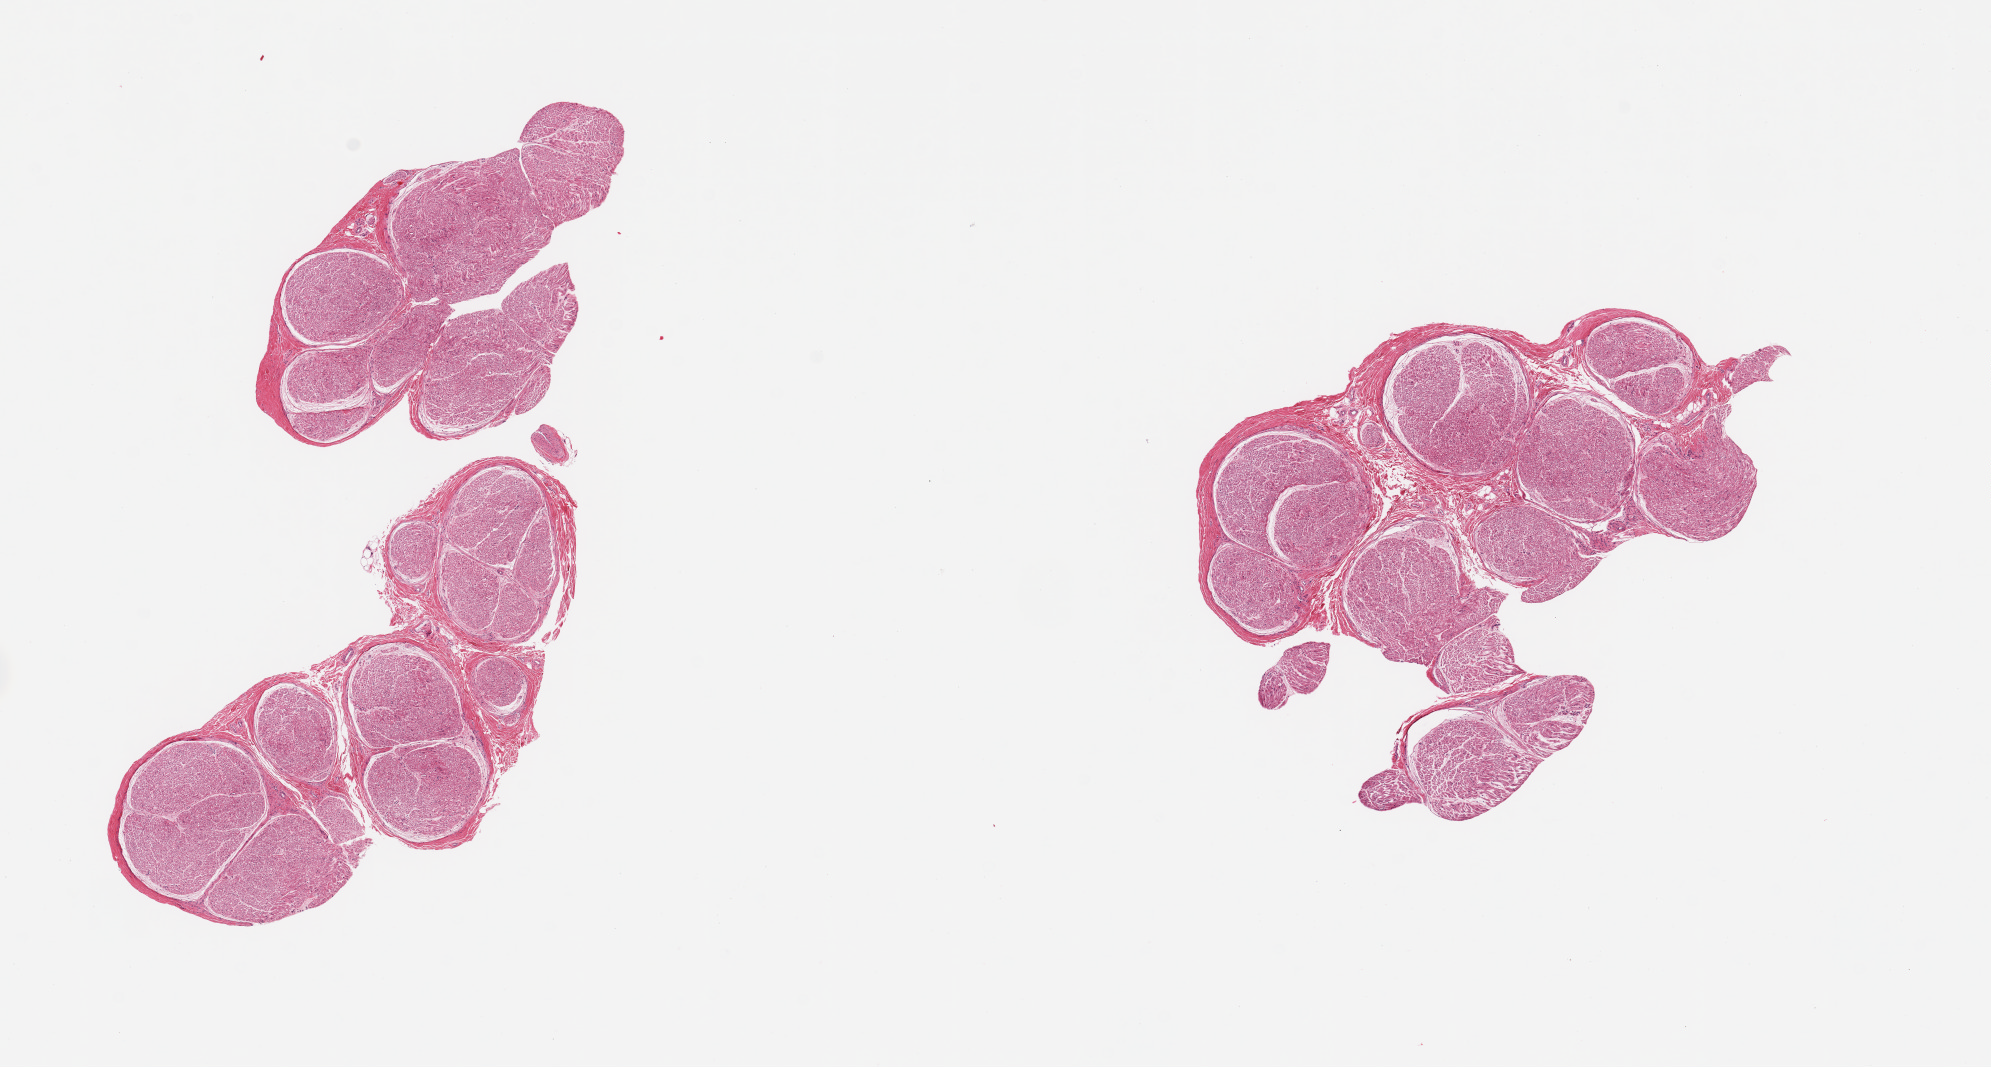
Haematoxylin and eosin whole-slide image, low-resolution overview of the scanned area, about 15.8 x 8.4 mm; PAXgene-fixed, paraffin-embedded tissue; target tissue: tibial nerve; tissue donor sample. Donor: male.
Pathologist's review note for this sample: 2 pieces; well trimmed.